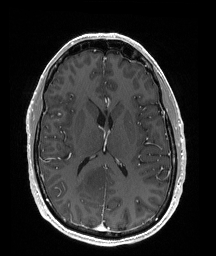
Brain MRI from a brain-tumour surgery series, one axial slice; slice 85 of 176 in the series (ordered by position); T1-weighted post-contrast; 216 × 256 image matrix, field of view 211 × 250 mm. From the clinical record (not read from this slice): histopathology: Oligodendroglioma; WHO grade: 2; IDH mutation: yes.
Outlined on this slice (outlined manually by an expert reader):
- tumour: box from (x=76, y=164) to (x=109, y=201) px